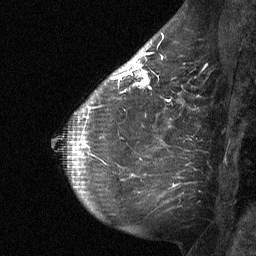
Breast MRI (dynamic contrast-enhanced), one sagittal slice. Position 44 of 64 along the scan axis. Dynamic contrast-enhanced study with each time point stored as its own series, time point 2 of 3 at this slice position (early post-contrast, ordered by acquisition time). 1.5 T. TE 4.8 ms, TR 27 ms. 2 mm slice thickness. 256 × 256 image matrix, field of view 200 × 200 mm. Female patient, age 51 years. Case-level facts recorded for this patient, not image findings: setting: breast cancer imaged before/during neoadjuvant chemotherapy; receptor status: HR-positive, HER2-negative.
Annotated regions visible in this slice (semi-automatic segmentation, software-assisted and operator-edited):
- analysis volume of interest (the breast-tissue region the enhancement analysis was run in; not a lesion): box from (x=112, y=46) to (x=168, y=101) px
- tumour enhancement mask (voxels above the 90 % enhancement threshold inside the analysis volume of interest): (x=112, y=52)–(x=150, y=87)